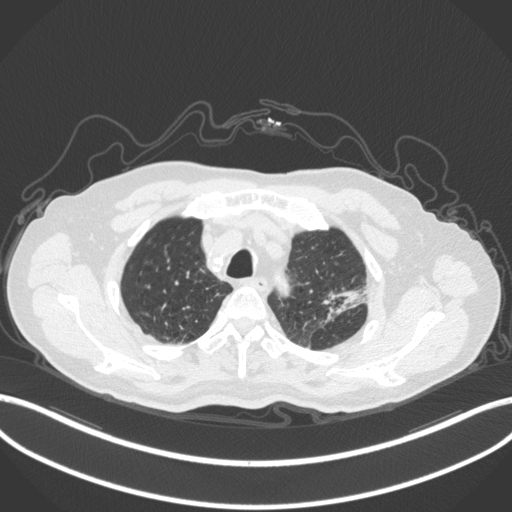
Chest CT, one axial slice. Position 249 of 331 along the scan axis. Reconstruction kernel B31f. 120 kVp. Lung window (W 1500 / L -600 HU). 1 mm slice thickness. 512 × 512 image matrix. Male patient, age 79 years. From the clinical record (not read from this slice): clinical TNM (as recorded): T2a N1 M1.
Outlined on this slice (rectangle marked by the reading radiologist):
- lung tumour (recorded histology: adenocarcinoma): bounding box (x1, y1, x2, y2) in pixels: (320, 285, 373, 324)